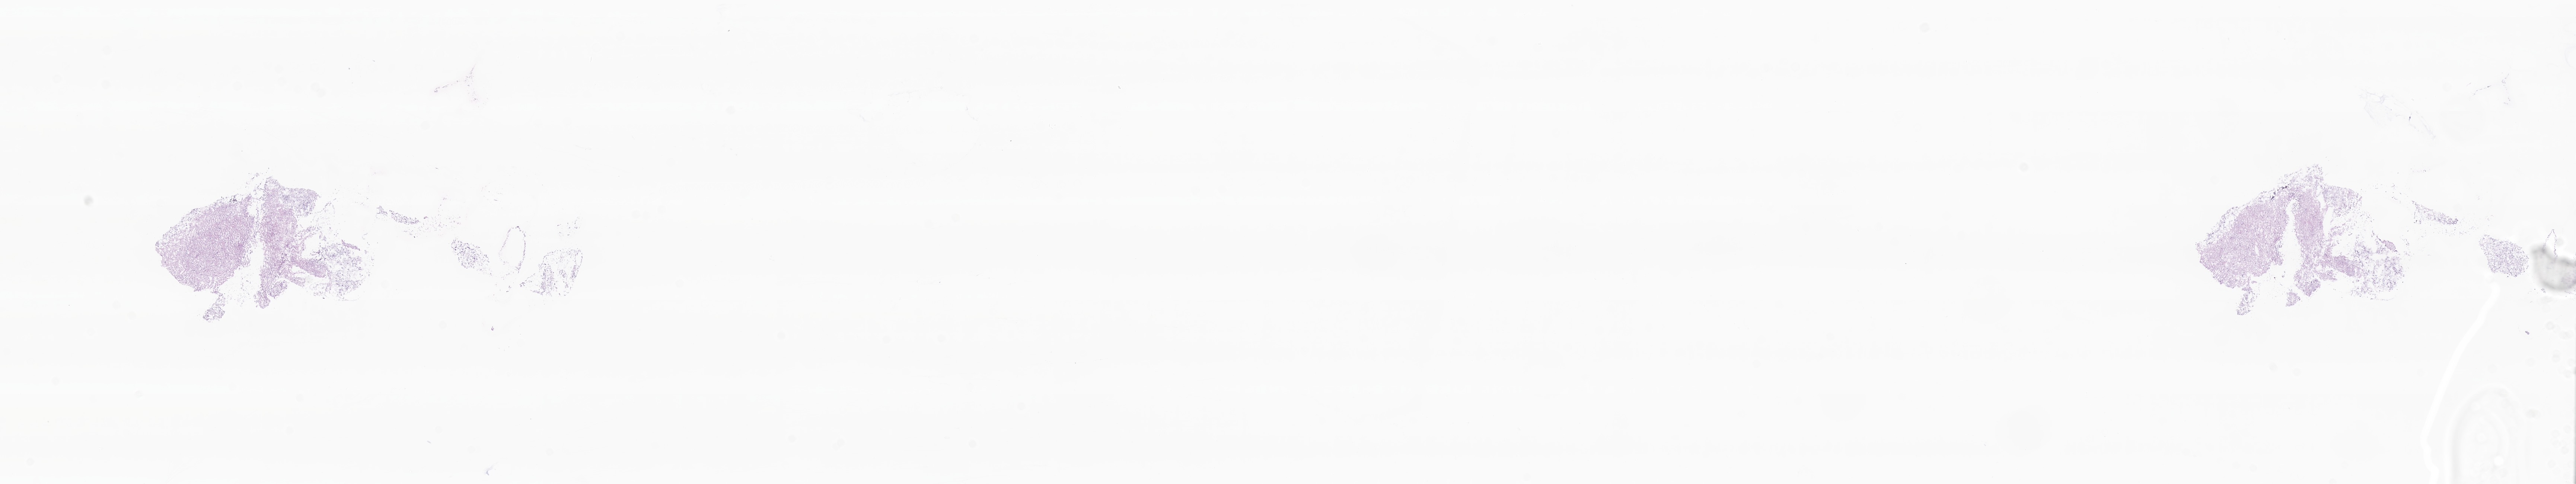
Whole-slide image, haematoxylin and eosin stain of tumor tissue from the brain, whole scanned area (about 29.2 x 5.5 mm) shown as a low-resolution overview, frozen section (OCT-embedded). Patient: male, age 121 months.
Diagnosis (ICD-O-3 morphology term): Glioma, malignant.